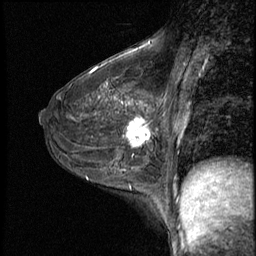
Breast MRI (dynamic contrast-enhanced), one sagittal slice; position 32 of 50 along the scan axis; 3 images stored at this slice position (order not interpretable as contrast timing); 1.5 T; TE 4.2 ms, TR 8.7 ms; 256 × 256 image matrix, field of view 180 × 180 mm. Patient: female, 43 years. From the clinical record (not read from this slice): setting: breast cancer imaged before/during neoadjuvant chemotherapy; receptor status: HR-positive, HER2-negative.
Annotated regions visible in this slice (semi-automatically segmented with operator editing):
- analysis volume of interest (the breast-tissue region the enhancement analysis was run in; not a lesion): bounding box [x1, y1, x2, y2] px = [122, 109, 159, 155]
- tumour enhancement mask (voxels above the 140 % enhancement threshold inside the analysis volume of interest): [127, 117, 151, 147]